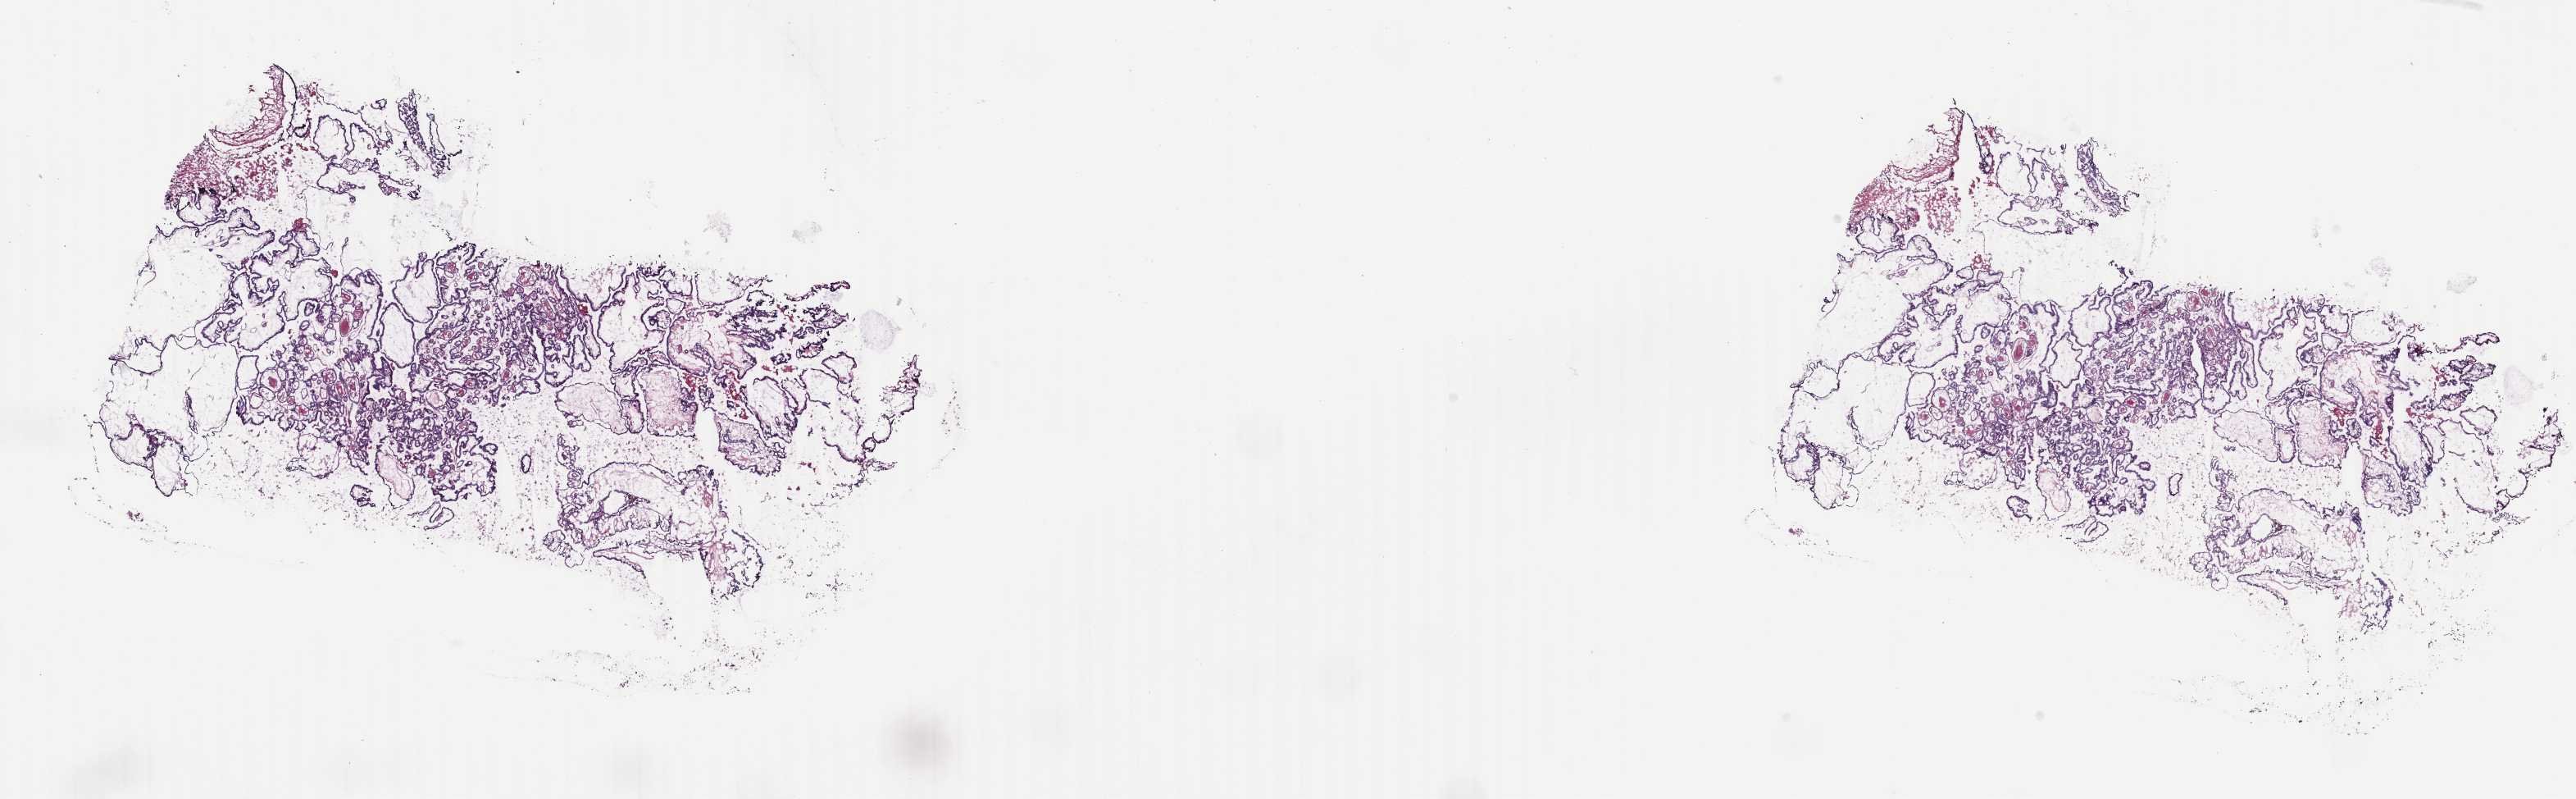
H&E-stained whole-slide image — low-resolution overview of the scanned area, about 25.0 x 7.7 mm, frozen section from the top of the tissue portion, sample: primary tumour, thyroid. Patient: male, age at initial diagnosis 47 years. Slide review estimates, as recorded: tumour cells 90%, tumour nuclei 95%, normal cells 0%, stromal cells 10%, necrosis 0%. Infiltration values recorded for this section: lymphocyte infiltration 0%, monocyte infiltration 0%, neutrophil infiltration 0%.
Histologic diagnosis: Papillary adenocarcinoma, NOS (thyroid gland). Lymph nodes positive (case pathology): 1 of 1 examined. TNM: T2 N1a M0. AJCC pathologic stage: III (7th edition).